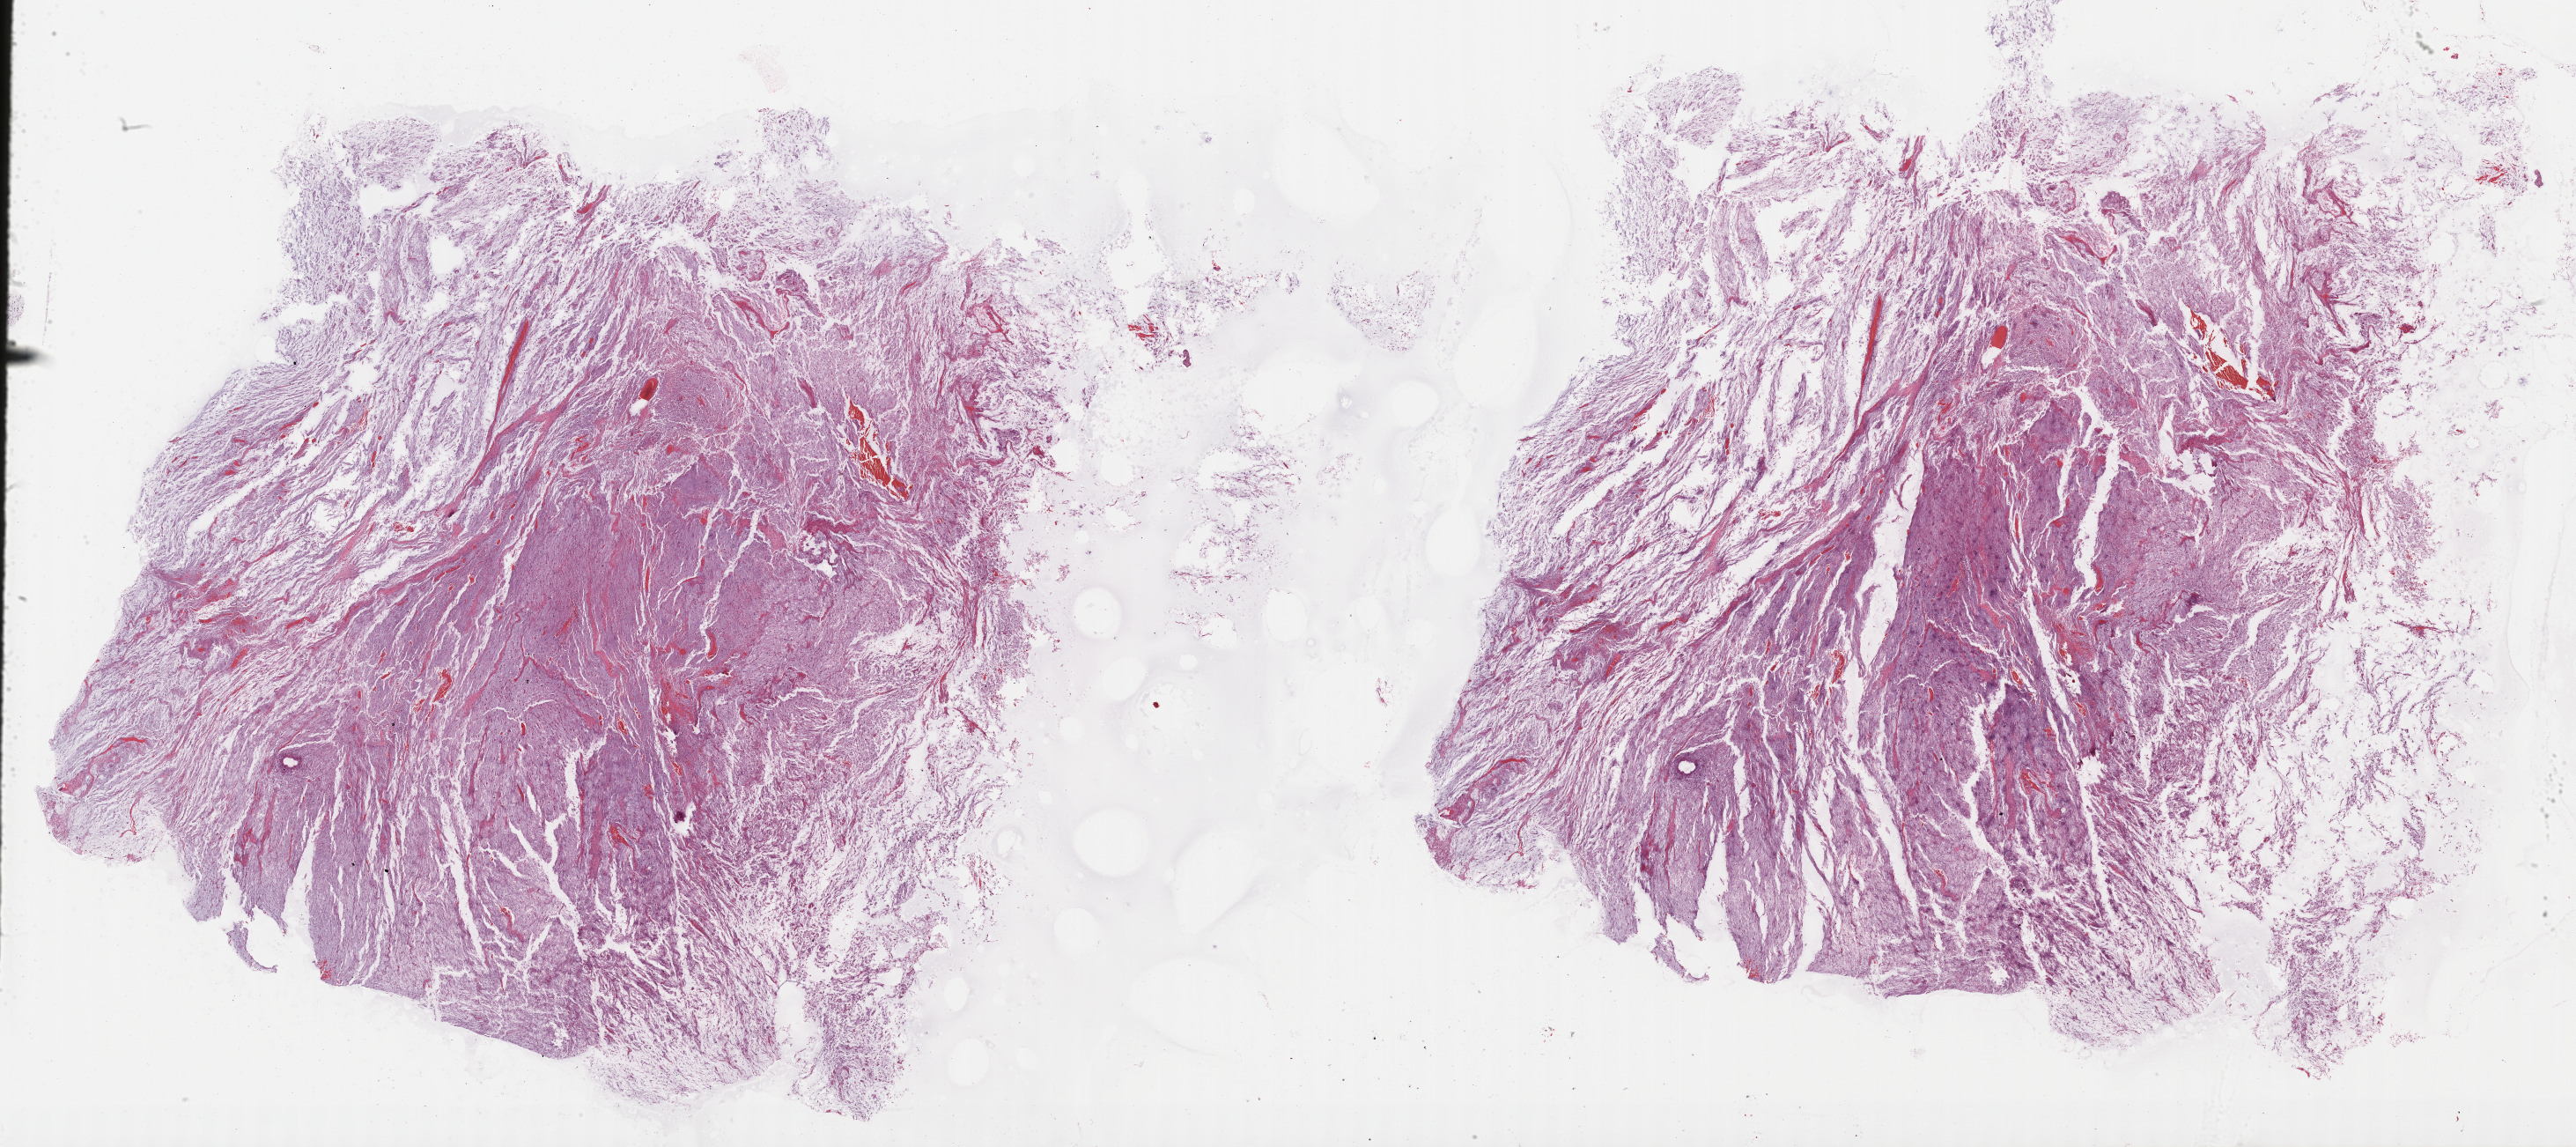
H&E whole-slide image, shown as a low-resolution overview of the whole scanned area (about 47.3 x 21.1 mm, acquisition: 40x scan). Formalin-fixed paraffin-embedded (FFPE) diagnostic section. Connective, subcutaneous and other soft tissues, primary tumour sample. Male patient; age at initial diagnosis 59 years.
Histologic diagnosis: Fibromyxosarcoma.